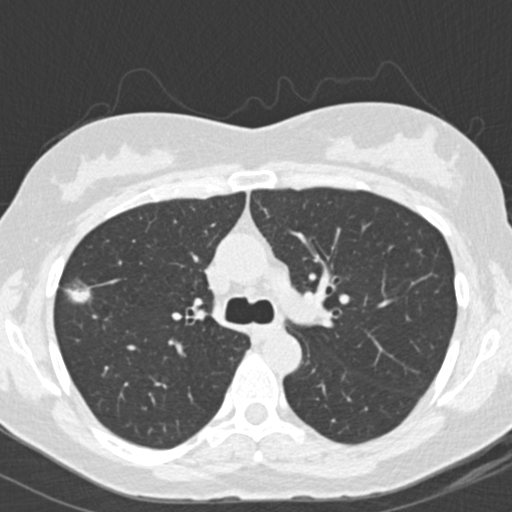
Low-dose screening chest CT, one axial slice; slice 109 of 157 in the series (ordered by position); reconstruction kernel B30f; lung window (W 1500 / L -600 HU); 2 mm slice thickness; 512 × 512 image matrix, field of view 290 × 290 mm.
Annotated regions visible in this slice (expert manual segmentation):
- lesion 1 (tumor, upper lobe of right lung): bounding box <65,285,91,303> (left, top, right, bottom; pixels)